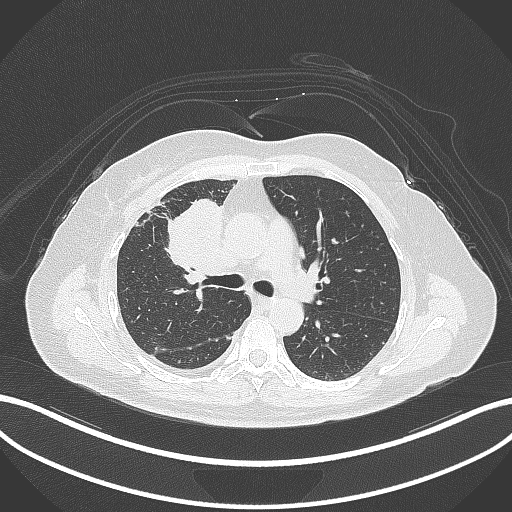
Chest CT, one axial slice; position 177 of 305 along the scan axis; reconstruction kernel B70f; 120 kVp; lung window (W 1500 / L -600 HU); 1 mm slice thickness; 512 × 512 image matrix, field of view 400 × 400 mm. Female patient, age 52 years. Case-level facts recorded for this patient, not image findings: clinical TNM (as recorded): T3 N1 M1.
Outlined on this slice (bounding box drawn by a radiologist):
- lung tumour (recorded histology: adenocarcinoma): bounding box [x1, y1, x2, y2] px = [162, 196, 226, 278]